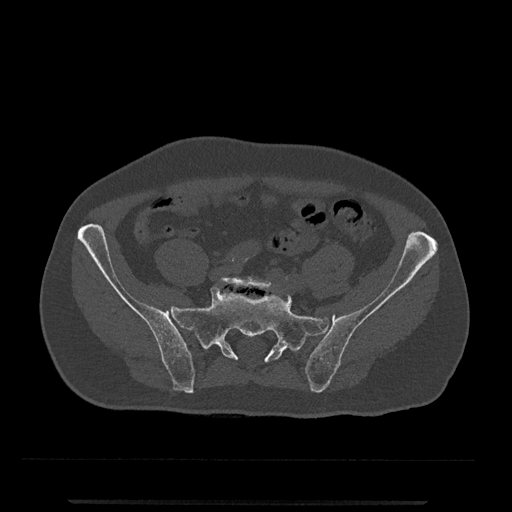
CT including the spine, one axial slice. Position 16 of 797 along the scan axis. 120 kVp. Bone window (W 1800 / L 400 HU). 0.5 mm slice thickness. 512 × 512 image matrix, field of view 419 × 419 mm. Male patient, age 63 years. Case-level facts recorded for this patient, not image findings: primary cancer: prostate.
Structures marked on this image (semi-automatically segmented with operator editing):
- L5 vertebra: box from (x=220, y=276) to (x=274, y=291) px